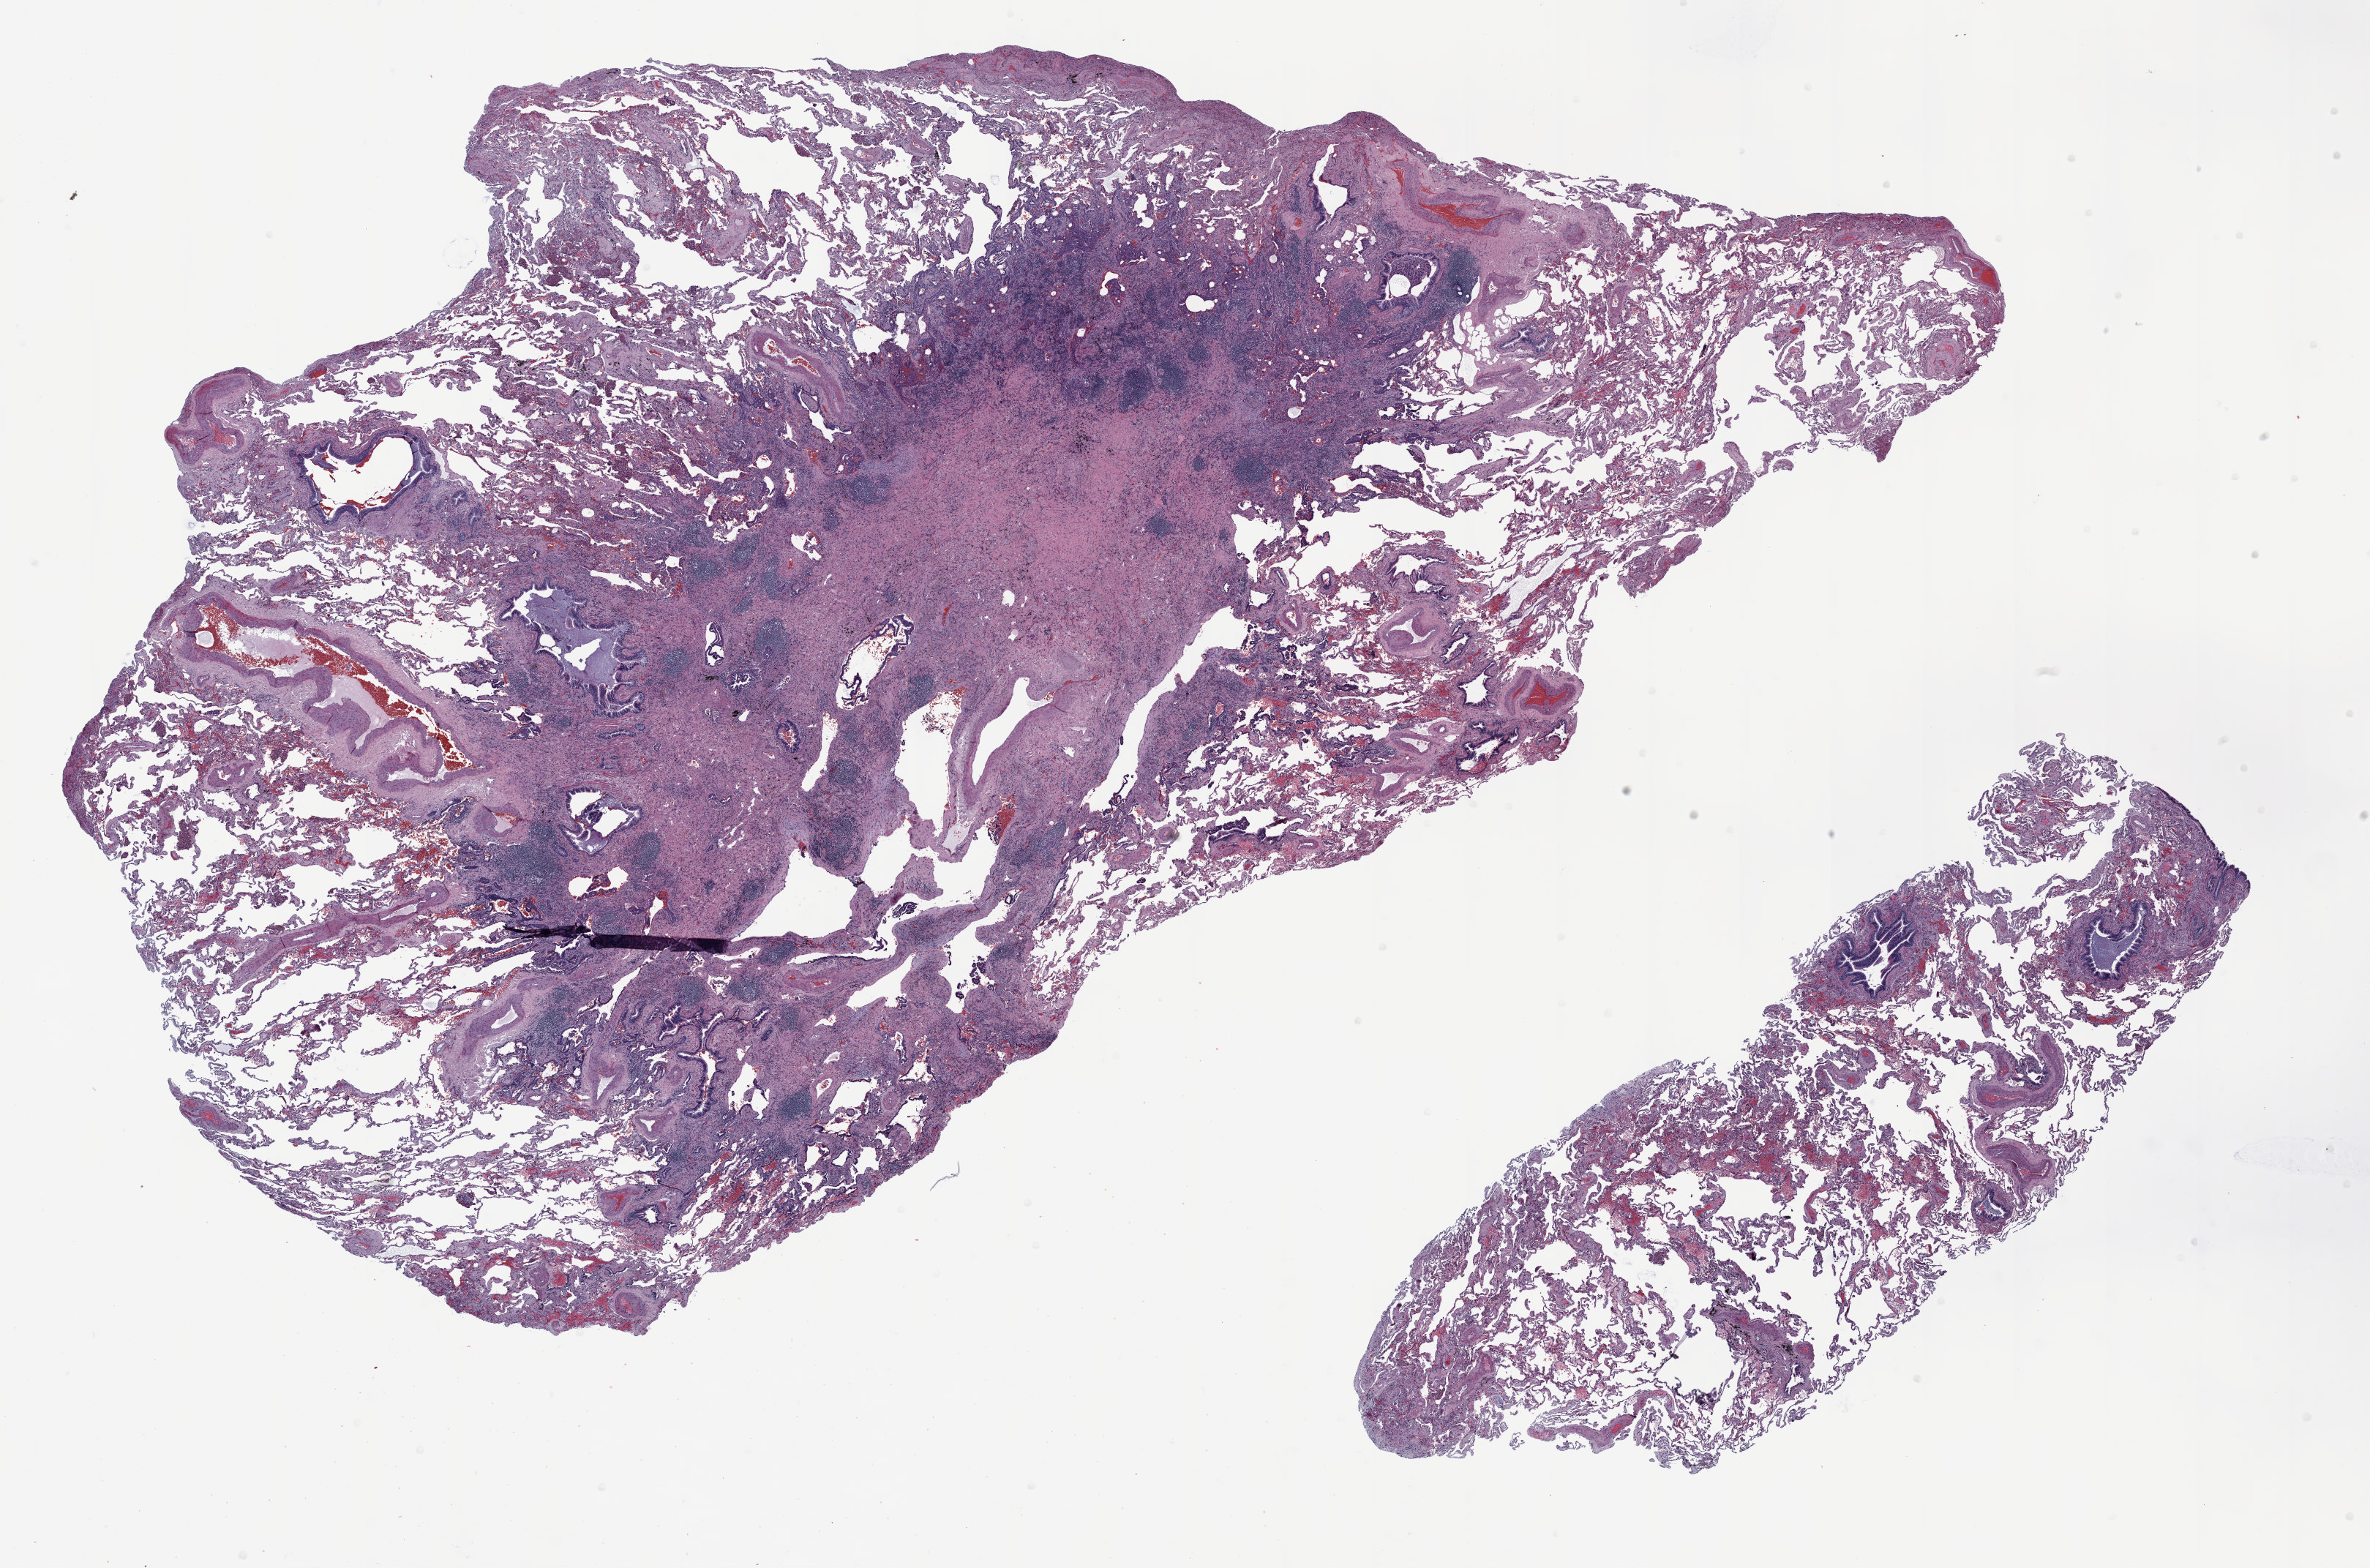
Whole-slide histology image, Hematoxylin and eosin (H&E) stained — shown as a low-resolution overview of the whole scanned area (about 26.0 x 17.2 mm); FFPE section; lung tissue. Female patient, aged 60 at enrolment. Current smoker at enrolment. Grade: well differentiated (G1).
Primary tumour location (clinical record): right upper lobe. Participant's lung-cancer diagnosis: Bronchiolo-alveolar adenocarcinoma, NOS. Tumour size (pathology): 11 mm. Stage (AJCC 6th edition): IA.